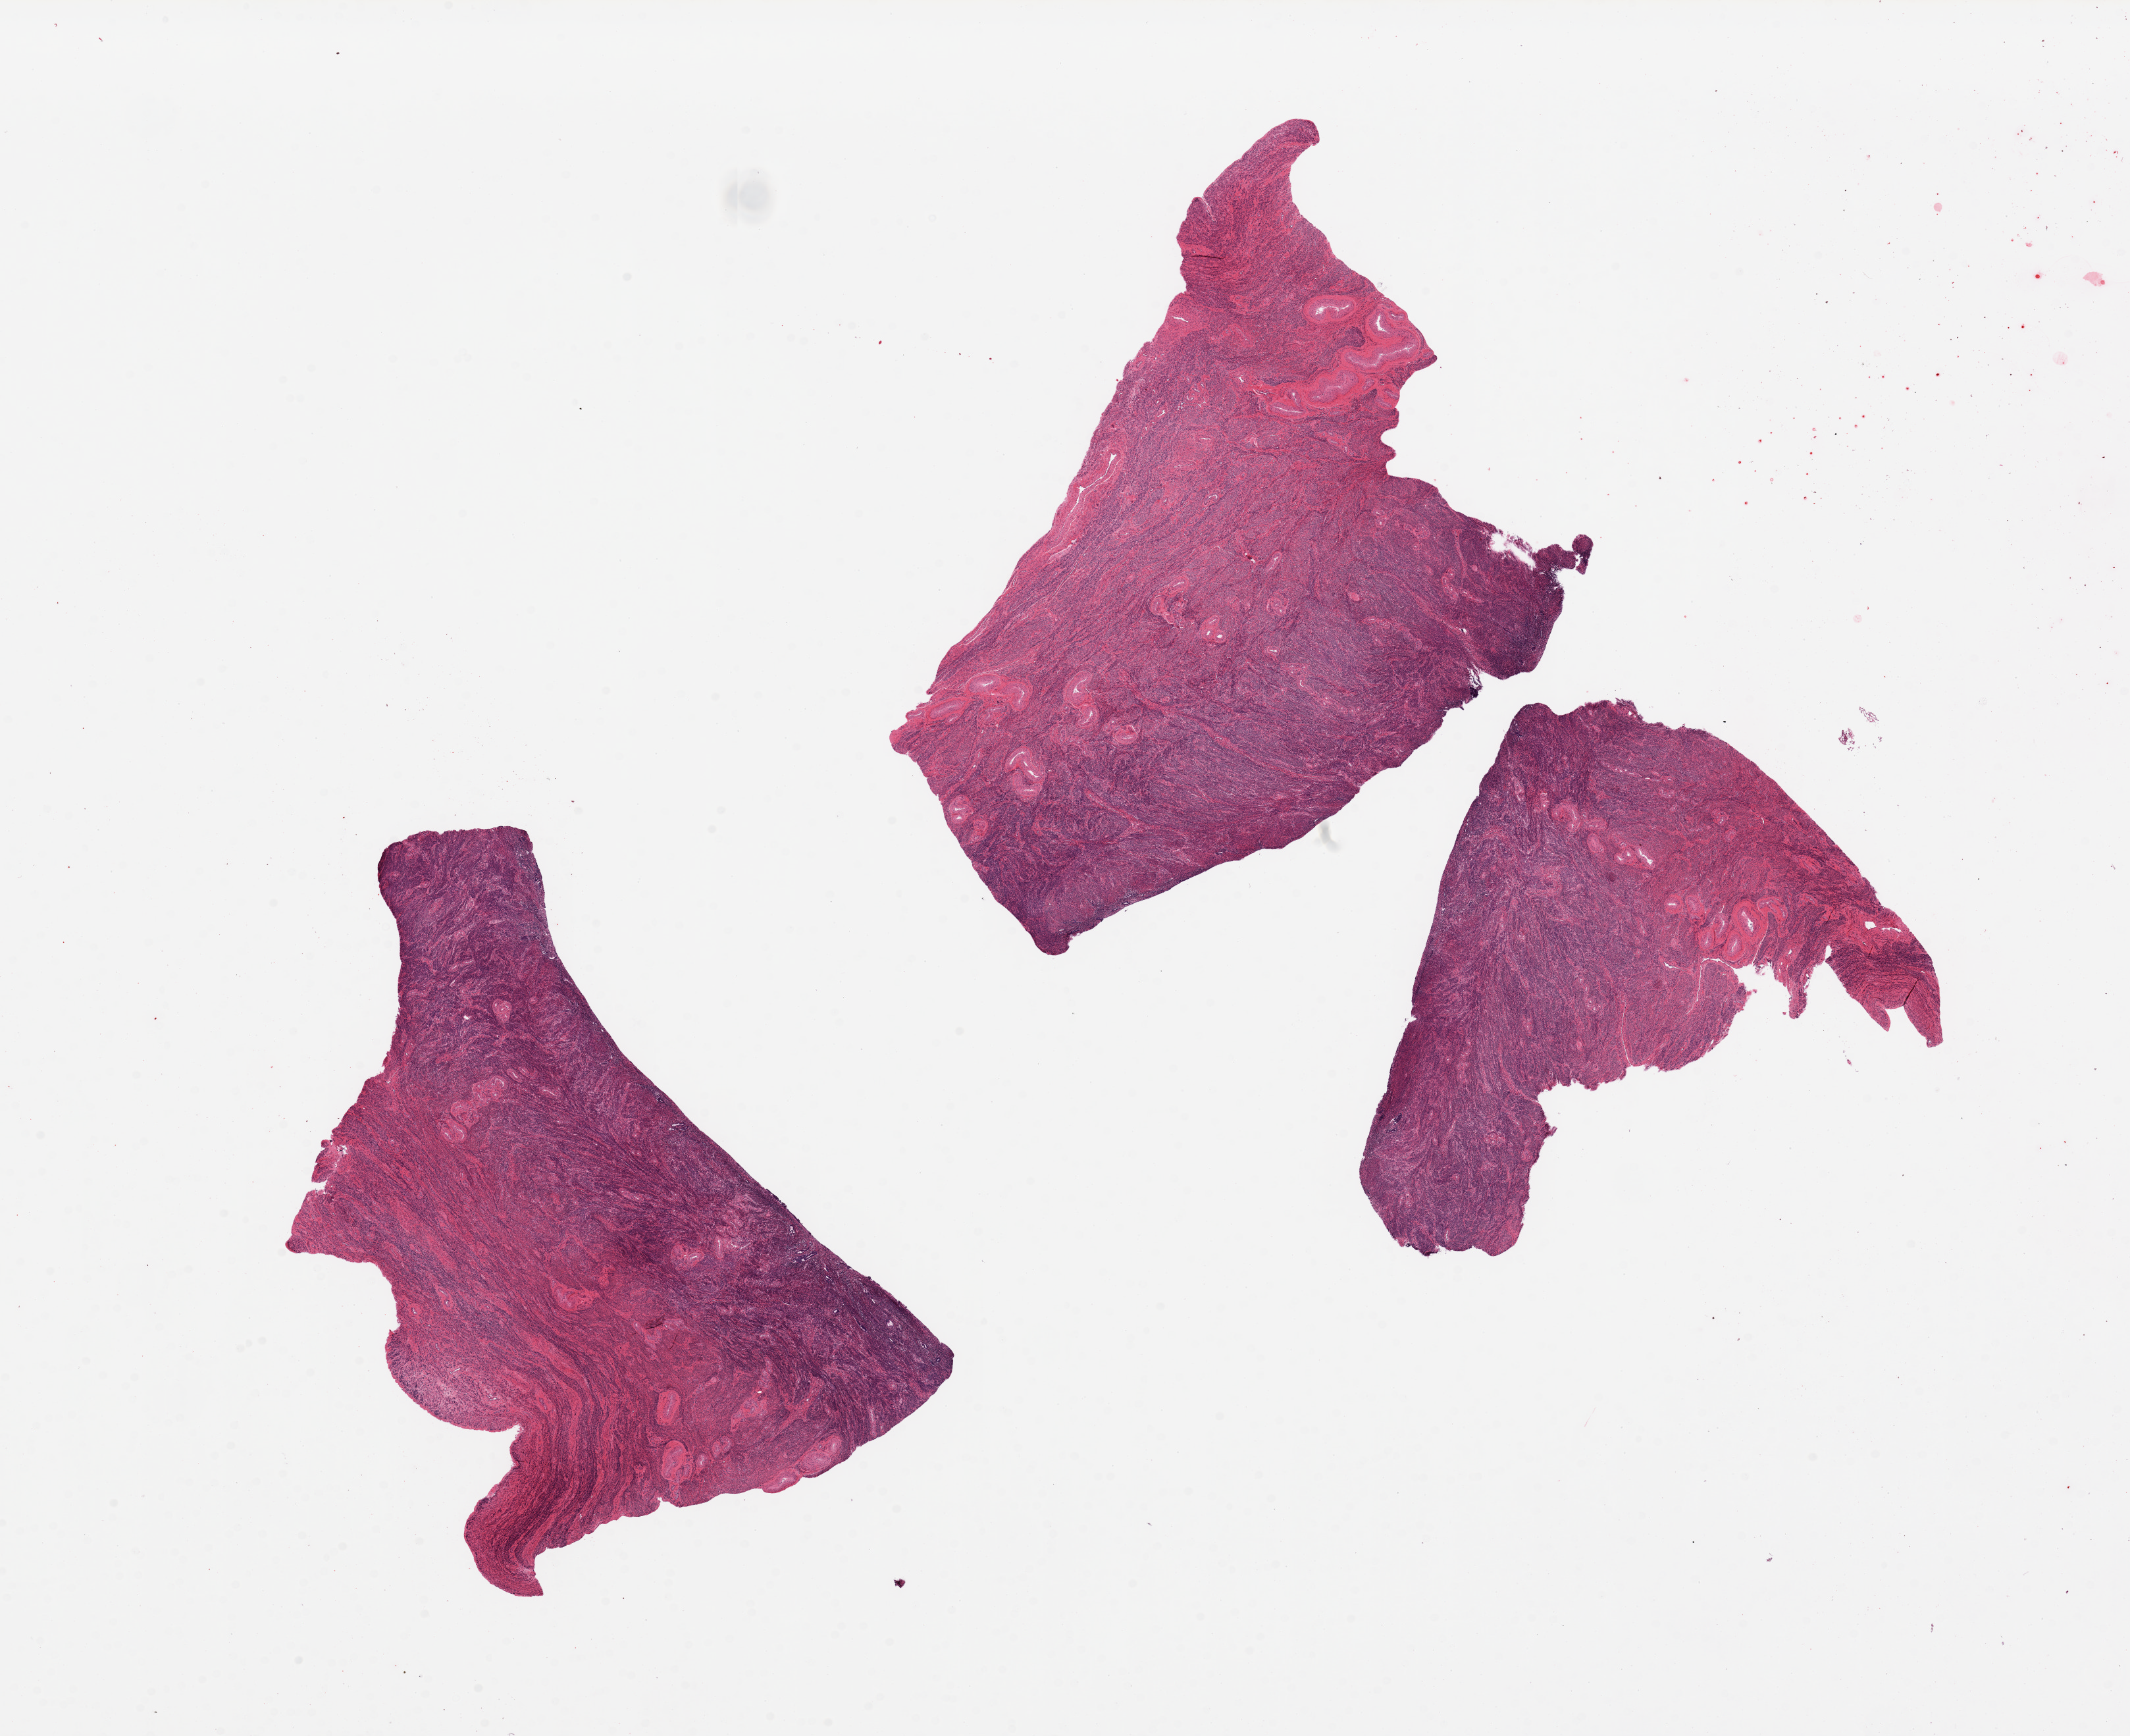
Whole-slide image, haematoxylin and eosin stain, brightfield — low-resolution overview of the scanned area, about 25.6 x 20.9 mm, PAXgene-fixed, paraffin-embedded tissue, sampled site (target tissue): uterus, tissue donor sample. Donor: female.
- review note (as recorded): 3 pieces